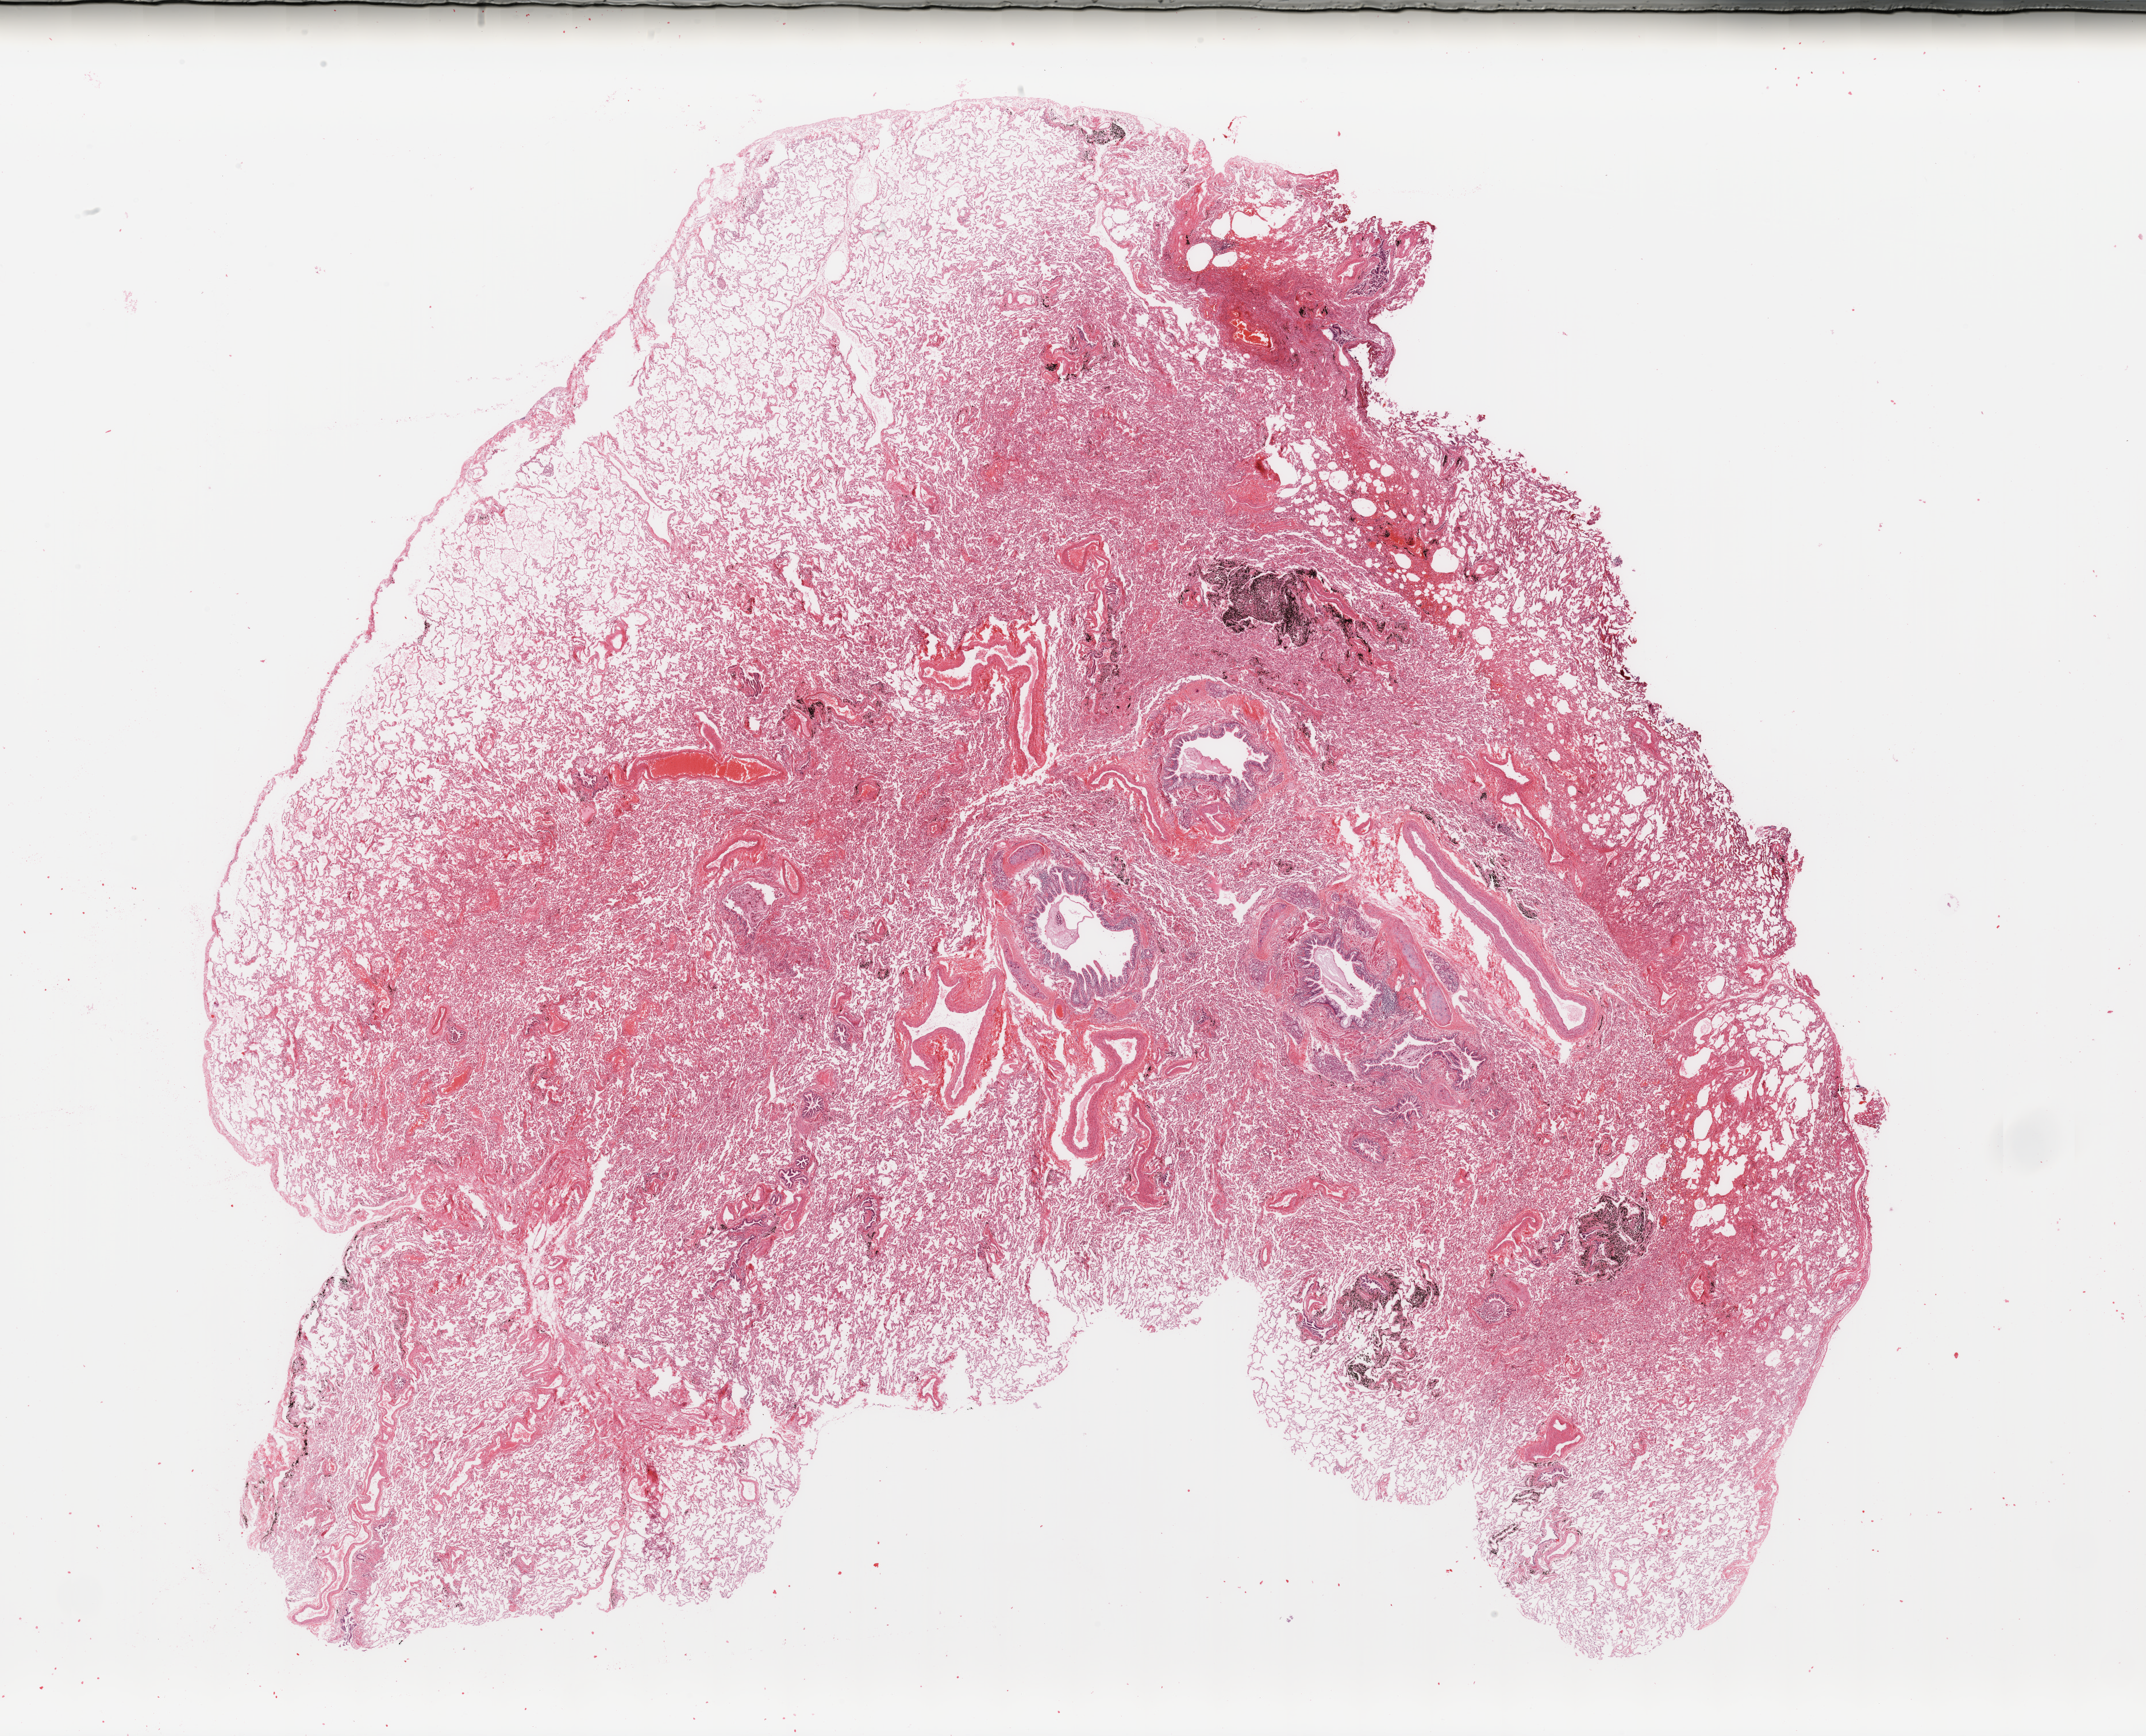
Hematoxylin and eosin (H&E) stained whole-slide image, low-resolution overview of the scanned area, about 29.5 x 23.9 mm (slide scanned at 20x); normal (non-tumour) tissue sample, lung. Male, 61 y/o.
* this section: normal (non-tumour) tissue from the same patient
* patient diagnosis: Adenocarcinoma, NOS